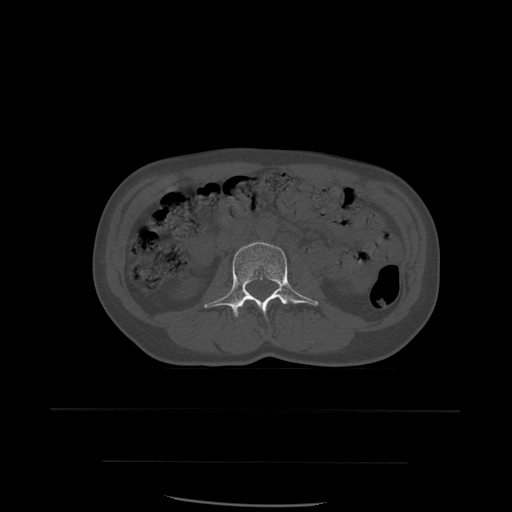
CT including the spine, one axial slice; slice 201 of 574 in the series (ordered by position); bone window (W 1800 / L 400 HU); 1.25 mm slice thickness; 512 × 512 image matrix, field of view 392 × 392 mm. Patient age 48 years. From the clinical record (not read from this slice): primary cancer: lung.
Outlined on this slice (semi-automatic segmentation, software-assisted and operator-edited):
- L3 vertebra: bounding box (x1, y1, x2, y2) in pixels: (204, 242, 318, 318)